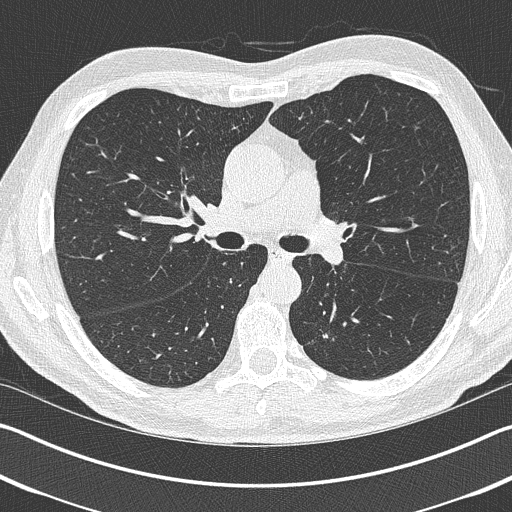
Axial slice from a low-dose chest CT screening exam, baseline screening round, lung window (W 1500 / L -600 HU), 1 mm slice thickness, 512 × 512 image matrix, field of view 340 × 340 mm. Male, age 69 years at enrolment.
Lesion marked by an expert reader, bounding box (x1, y1, x2, y2) in pixels: (303, 310, 358, 360). Screening reader's record for this exam (one nodule recorded; not confirmed to be the boxed lesion): non-calcified nodule or mass ≥4 mm, left upper lobe, 19 × 19 mm, spiculated (stellate) margins, pre-existing on the prior screen: yes. Lung cancer was diagnosed 202 days after this screen: non-small cell carcinoma, left lower lobe, stage IIIA (AJCC 6th edition), 20 mm at pathology.